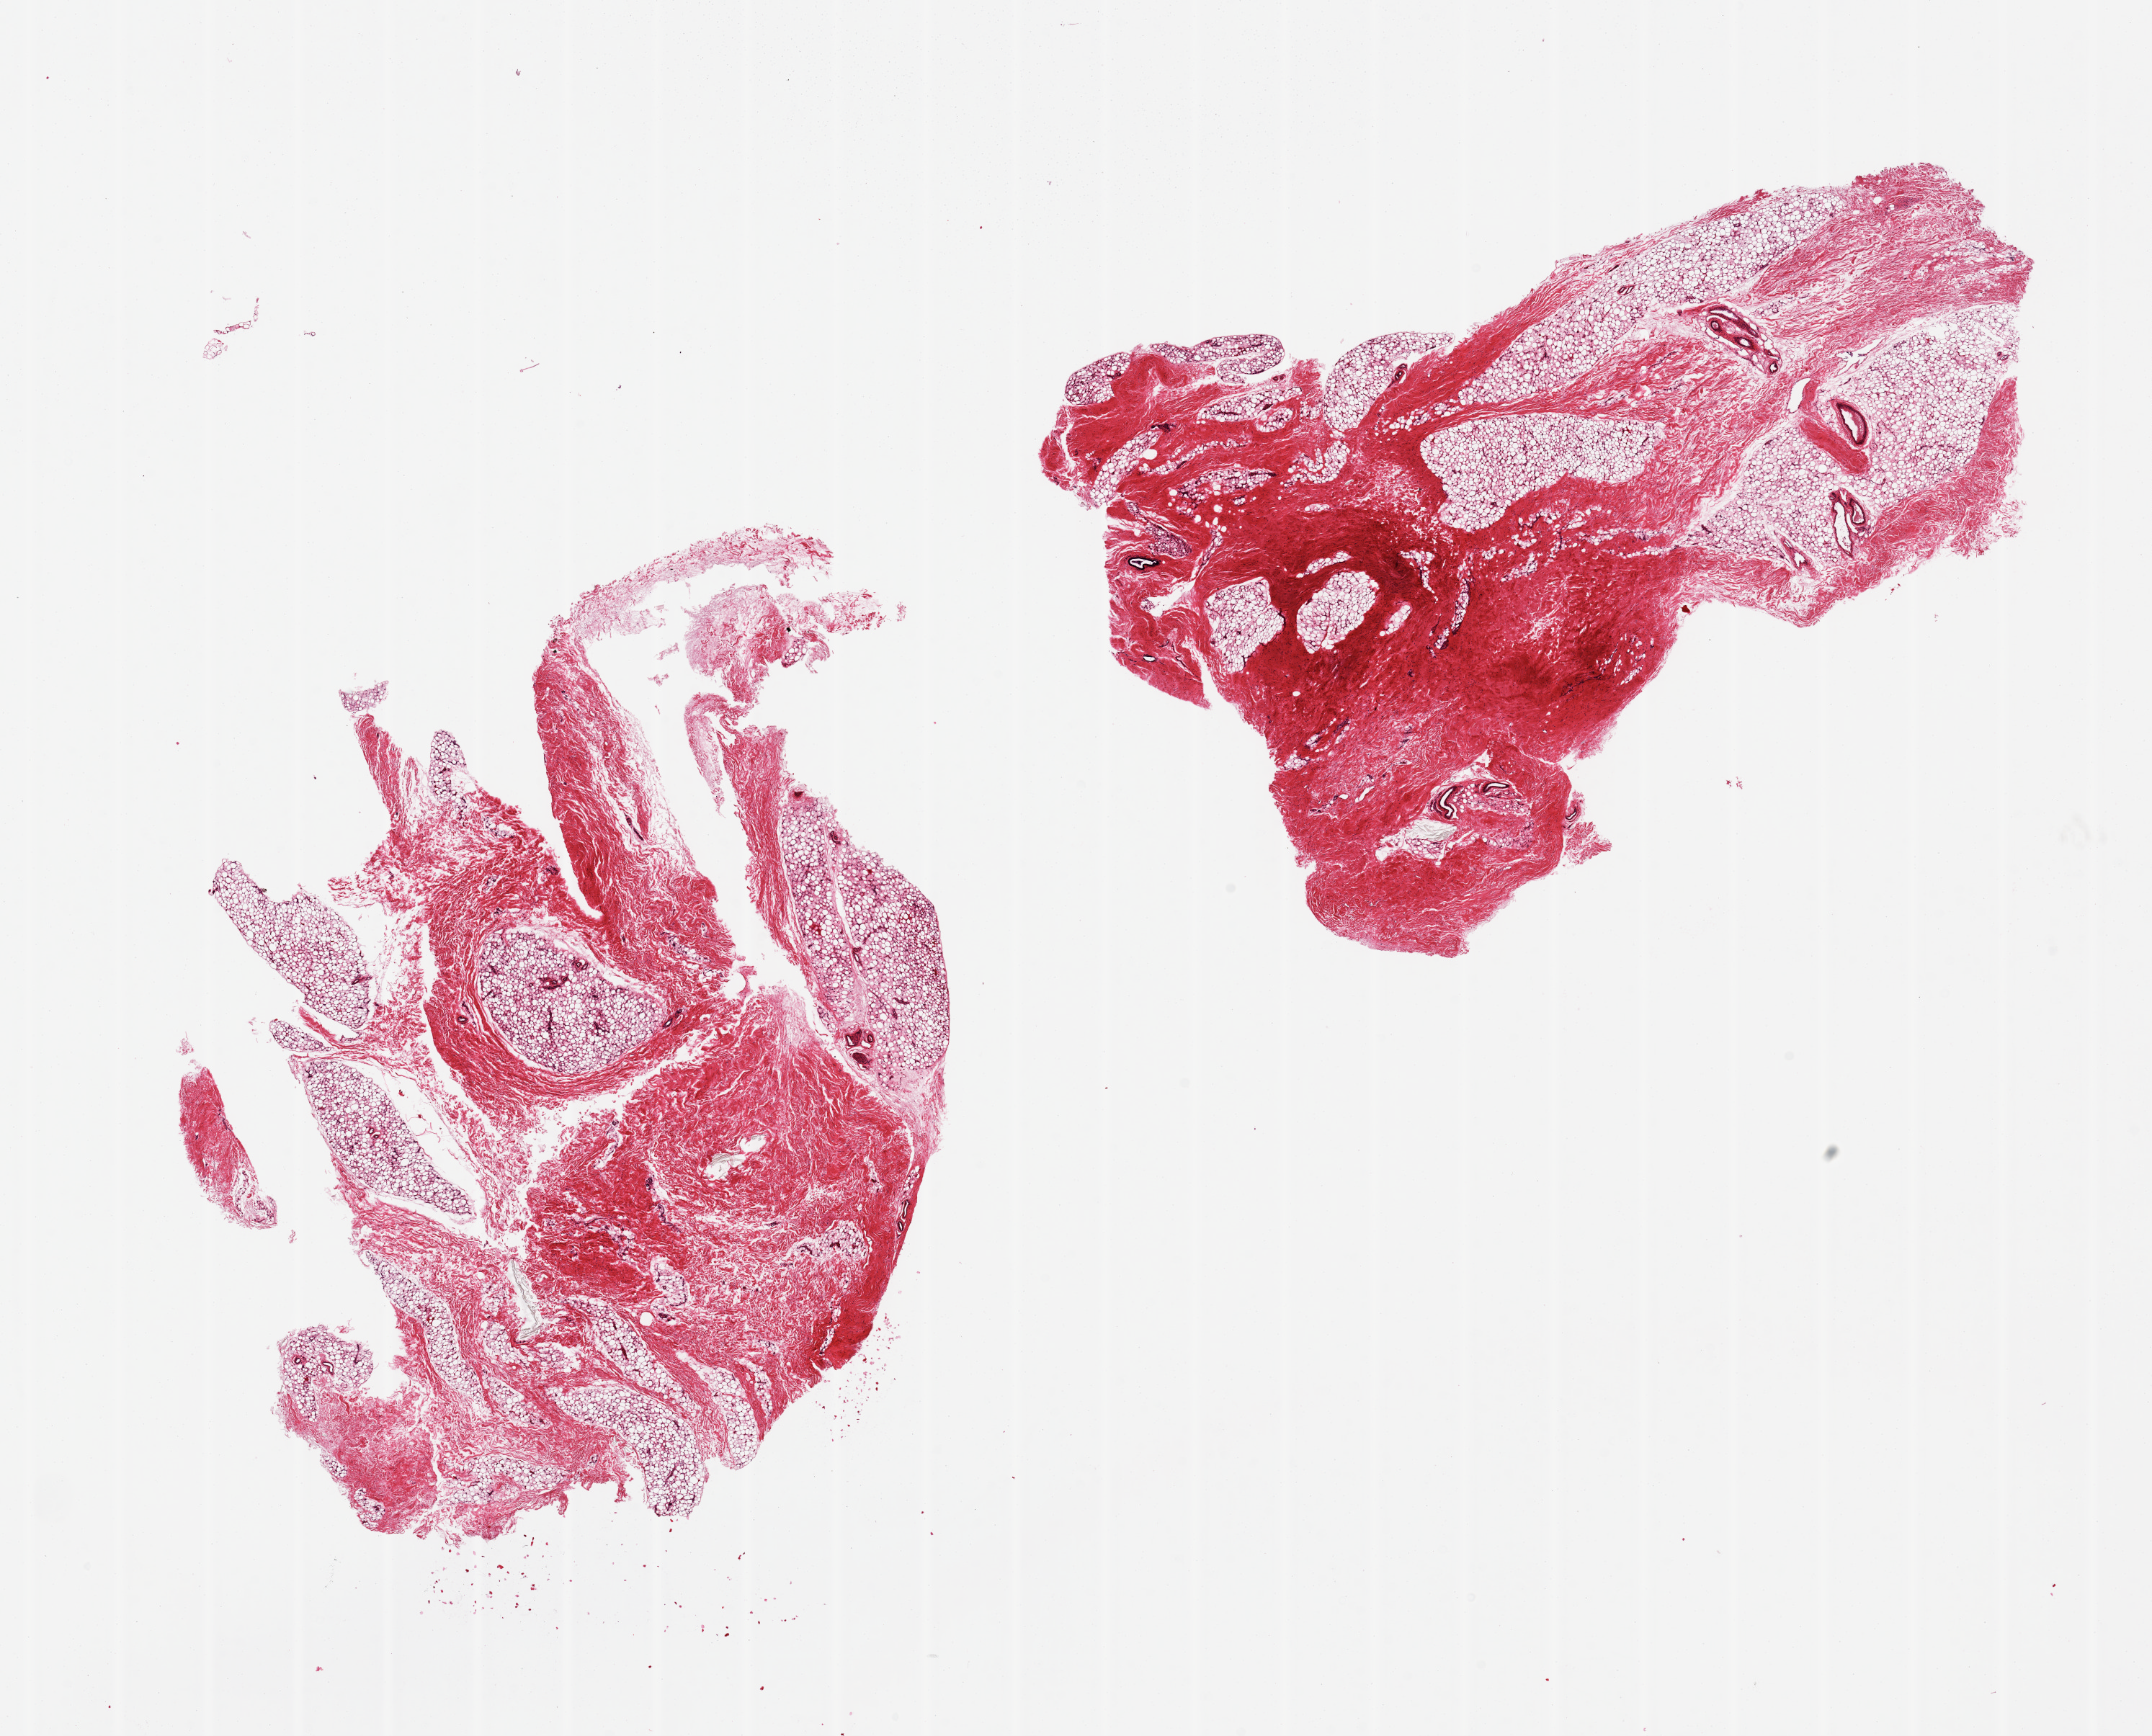
Digitized haematoxylin and eosin-stained section, a low-resolution overview of the entire scanned area, about 23.6 x 19.1 mm (from a 20x scan). PAXgene-fixed paraffin-embedded (PFPE) section. Sampled site (target tissue): breast. Tissue donor sample. Donor sex: male.
Review note (as recorded): 2 pieces; Largely fibroadipose; Rare duct.